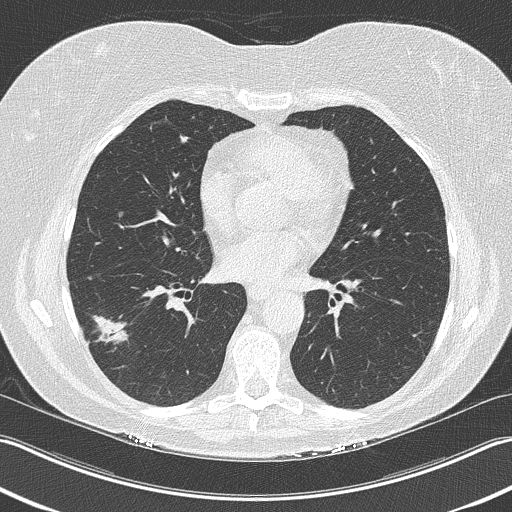
Low-dose screening chest CT, one axial slice. Slice 108 of 210 in the series (ordered by position). Lung window (W 1500 / L -600 HU). 2 mm slice thickness. 512 × 512 image matrix.
Outlined on this slice (outlined manually by an expert reader):
- lesion 1 (tumor, lower lobe of right lung): bounding box <92,315,129,345> (left, top, right, bottom; pixels)